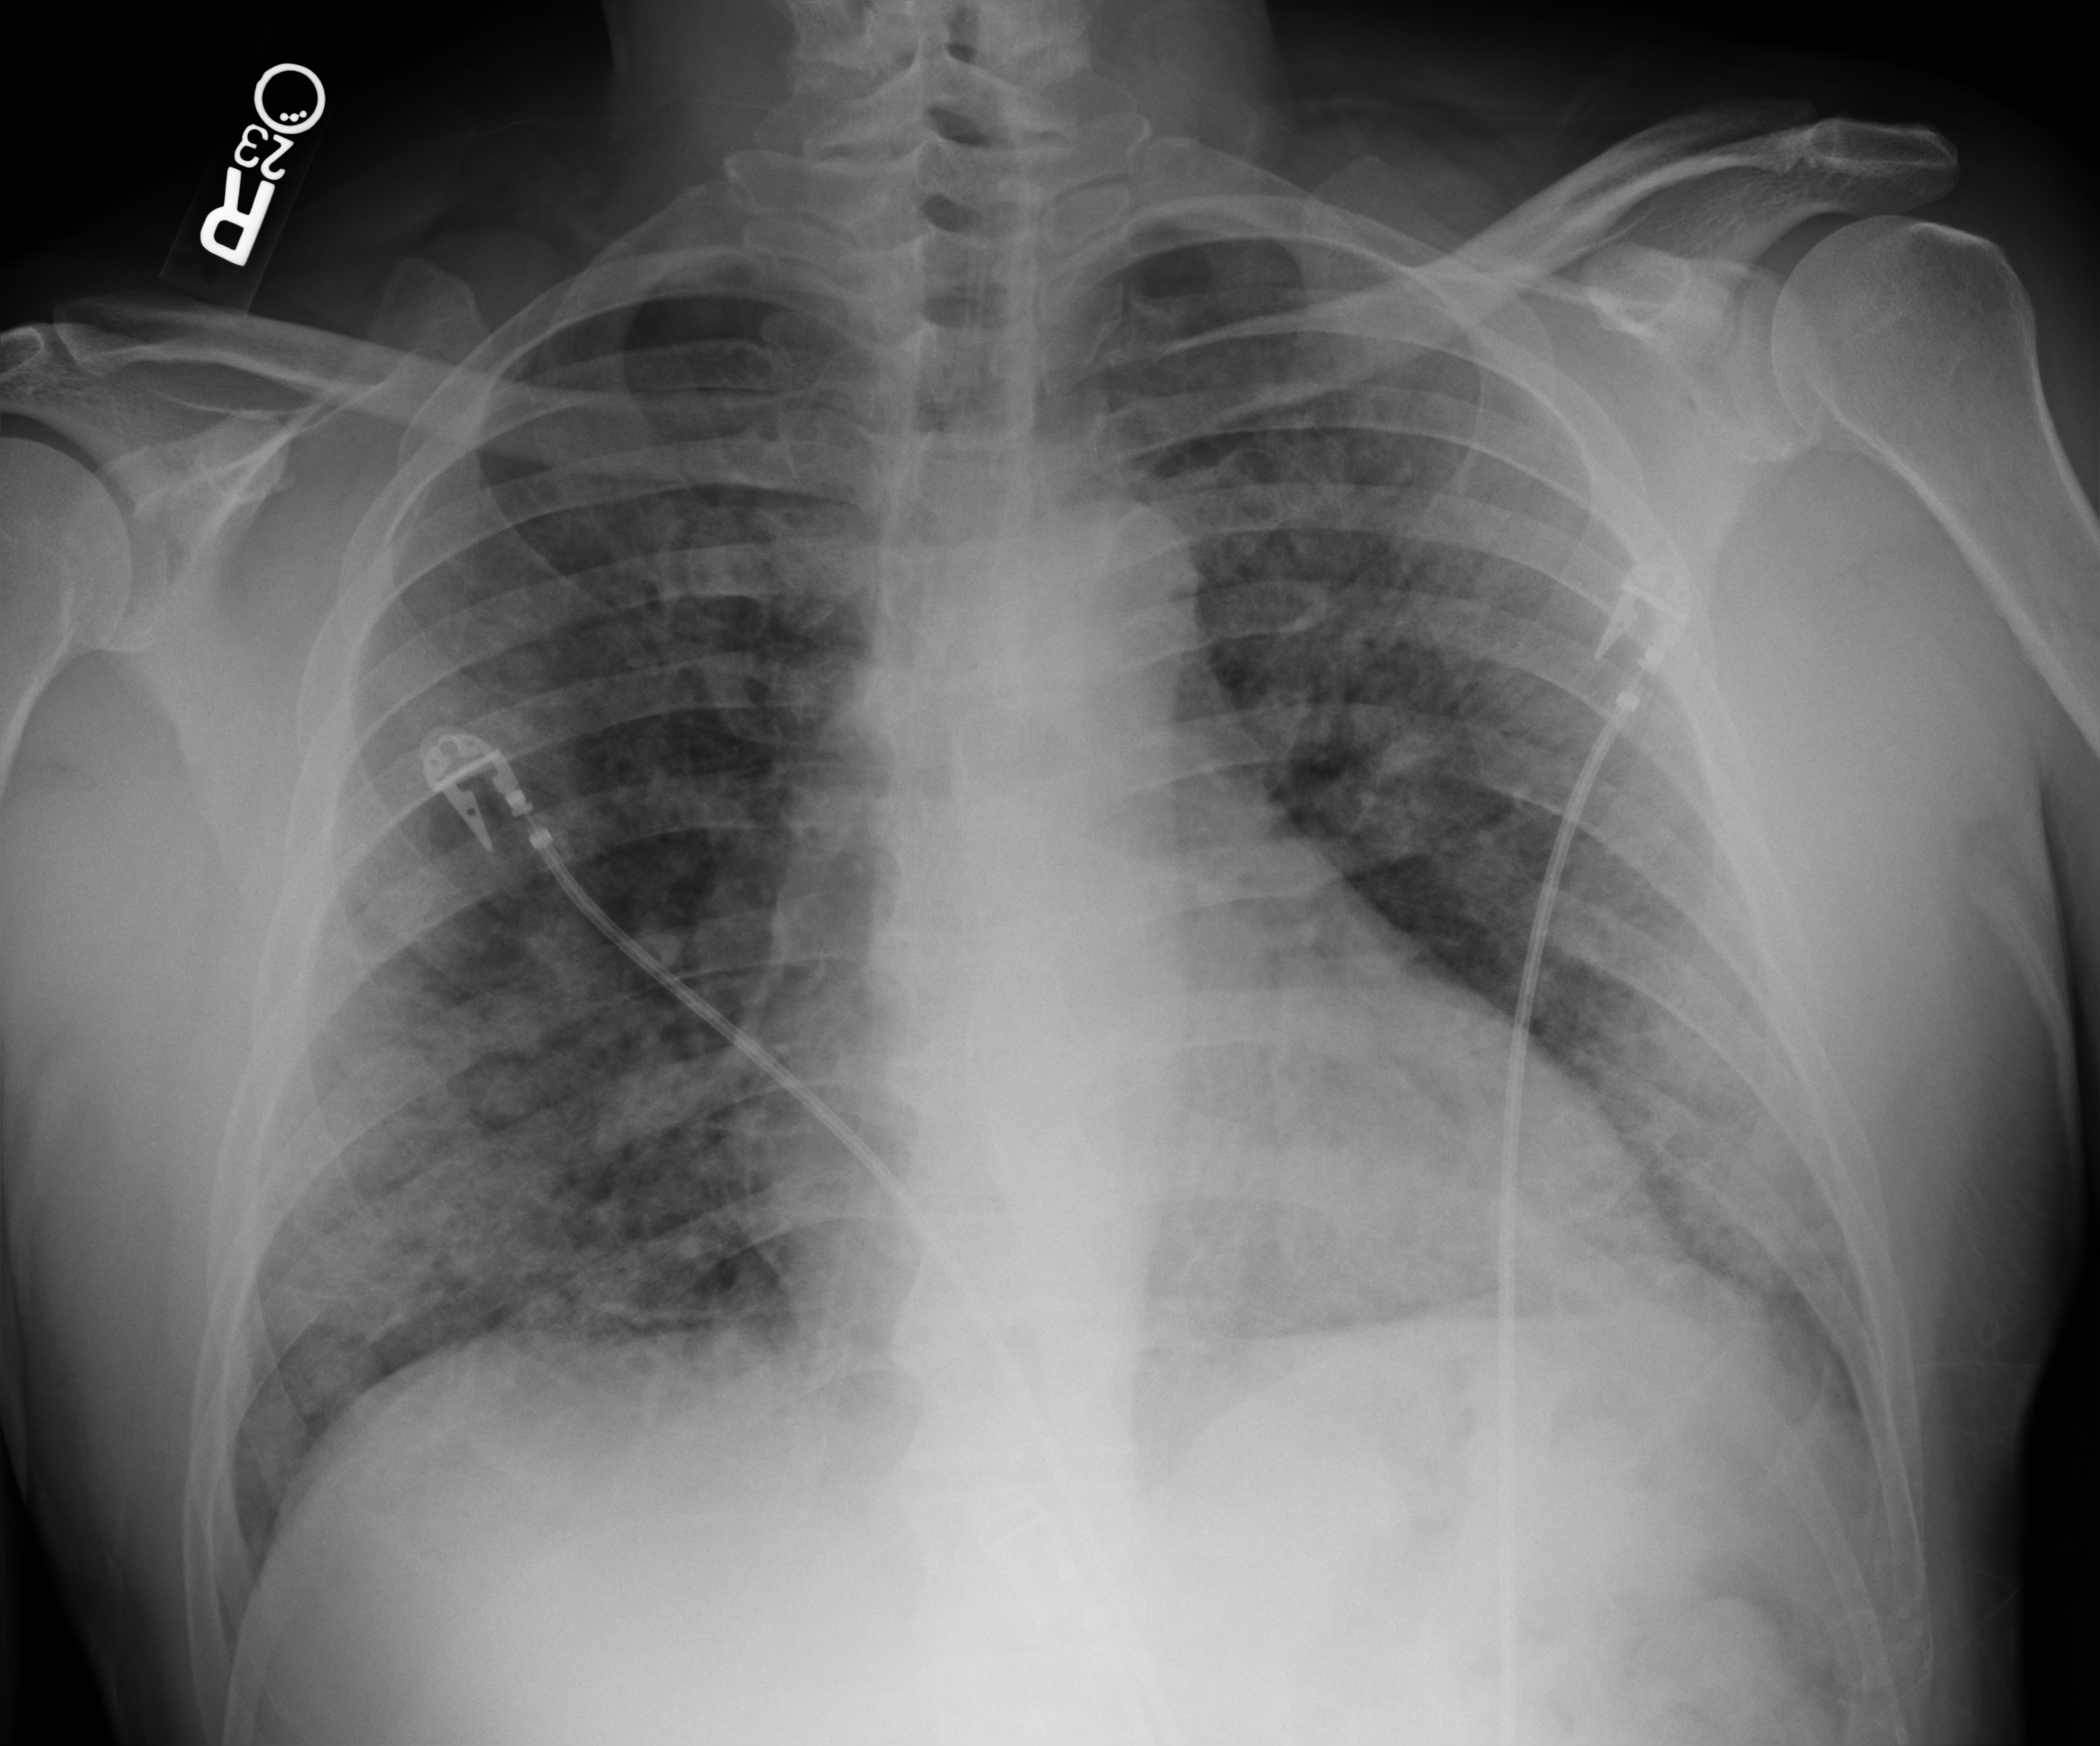
Chest X-ray (portable), anteroposterior (AP) projection. Male patient hospitalised with COVID-19, age 18–59 years.
Hospital-stay facts (about this admission, not read from this image; timing relative to this image not recorded):
- smoking status (admission record): never
- COPD (admission record): no
- hypertension (admission record): yes